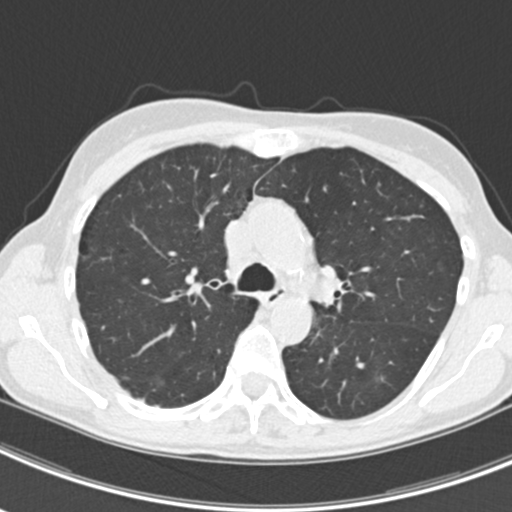
Axial slice from a low-dose chest CT screening exam. Second annual screen. Lung window (W 1500 / L -600 HU). 120 kVp. Female participant, aged 63 years at enrolment.
Expert-annotated lung lesion, box from (x=365, y=365) to (x=398, y=394) px. The screening reader recorded 9 non-calcified nodules or masses ≥4 mm on this exam; which of them this box marks is not recorded. Official screen result: positive, other. Participant outcome: lung cancer diagnosed 408 days after this screen — bronchiolo-alveolar adenocarcinoma, NOS, right upper lobe, right middle lobe, right lower lobe, left upper lobe, left lower lobe, moderately differentiated (G2), stage IV (AJCC 6th edition).